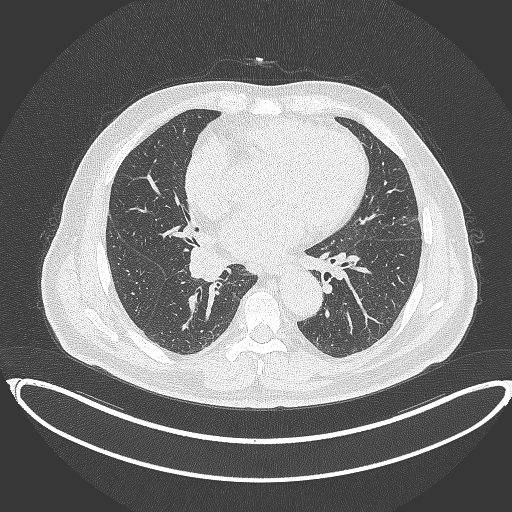
Chest CT, one axial slice. Slice 191 of 387 in the series (ordered by position). Reconstruction kernel B70f. 120 kVp. Lung window (W 1500 / L -600 HU). 512 × 512 image matrix, field of view 448 × 448 mm. Male patient, age 61 years. Case-level facts recorded for this patient, not image findings: clinical TNM (as recorded): T1b N1 M0.
Annotated regions visible in this slice (rectangle marked by the reading radiologist):
- lung tumour (recorded histology: squamous cell carcinoma): bounding box [x1, y1, x2, y2] px = [184, 241, 233, 285]